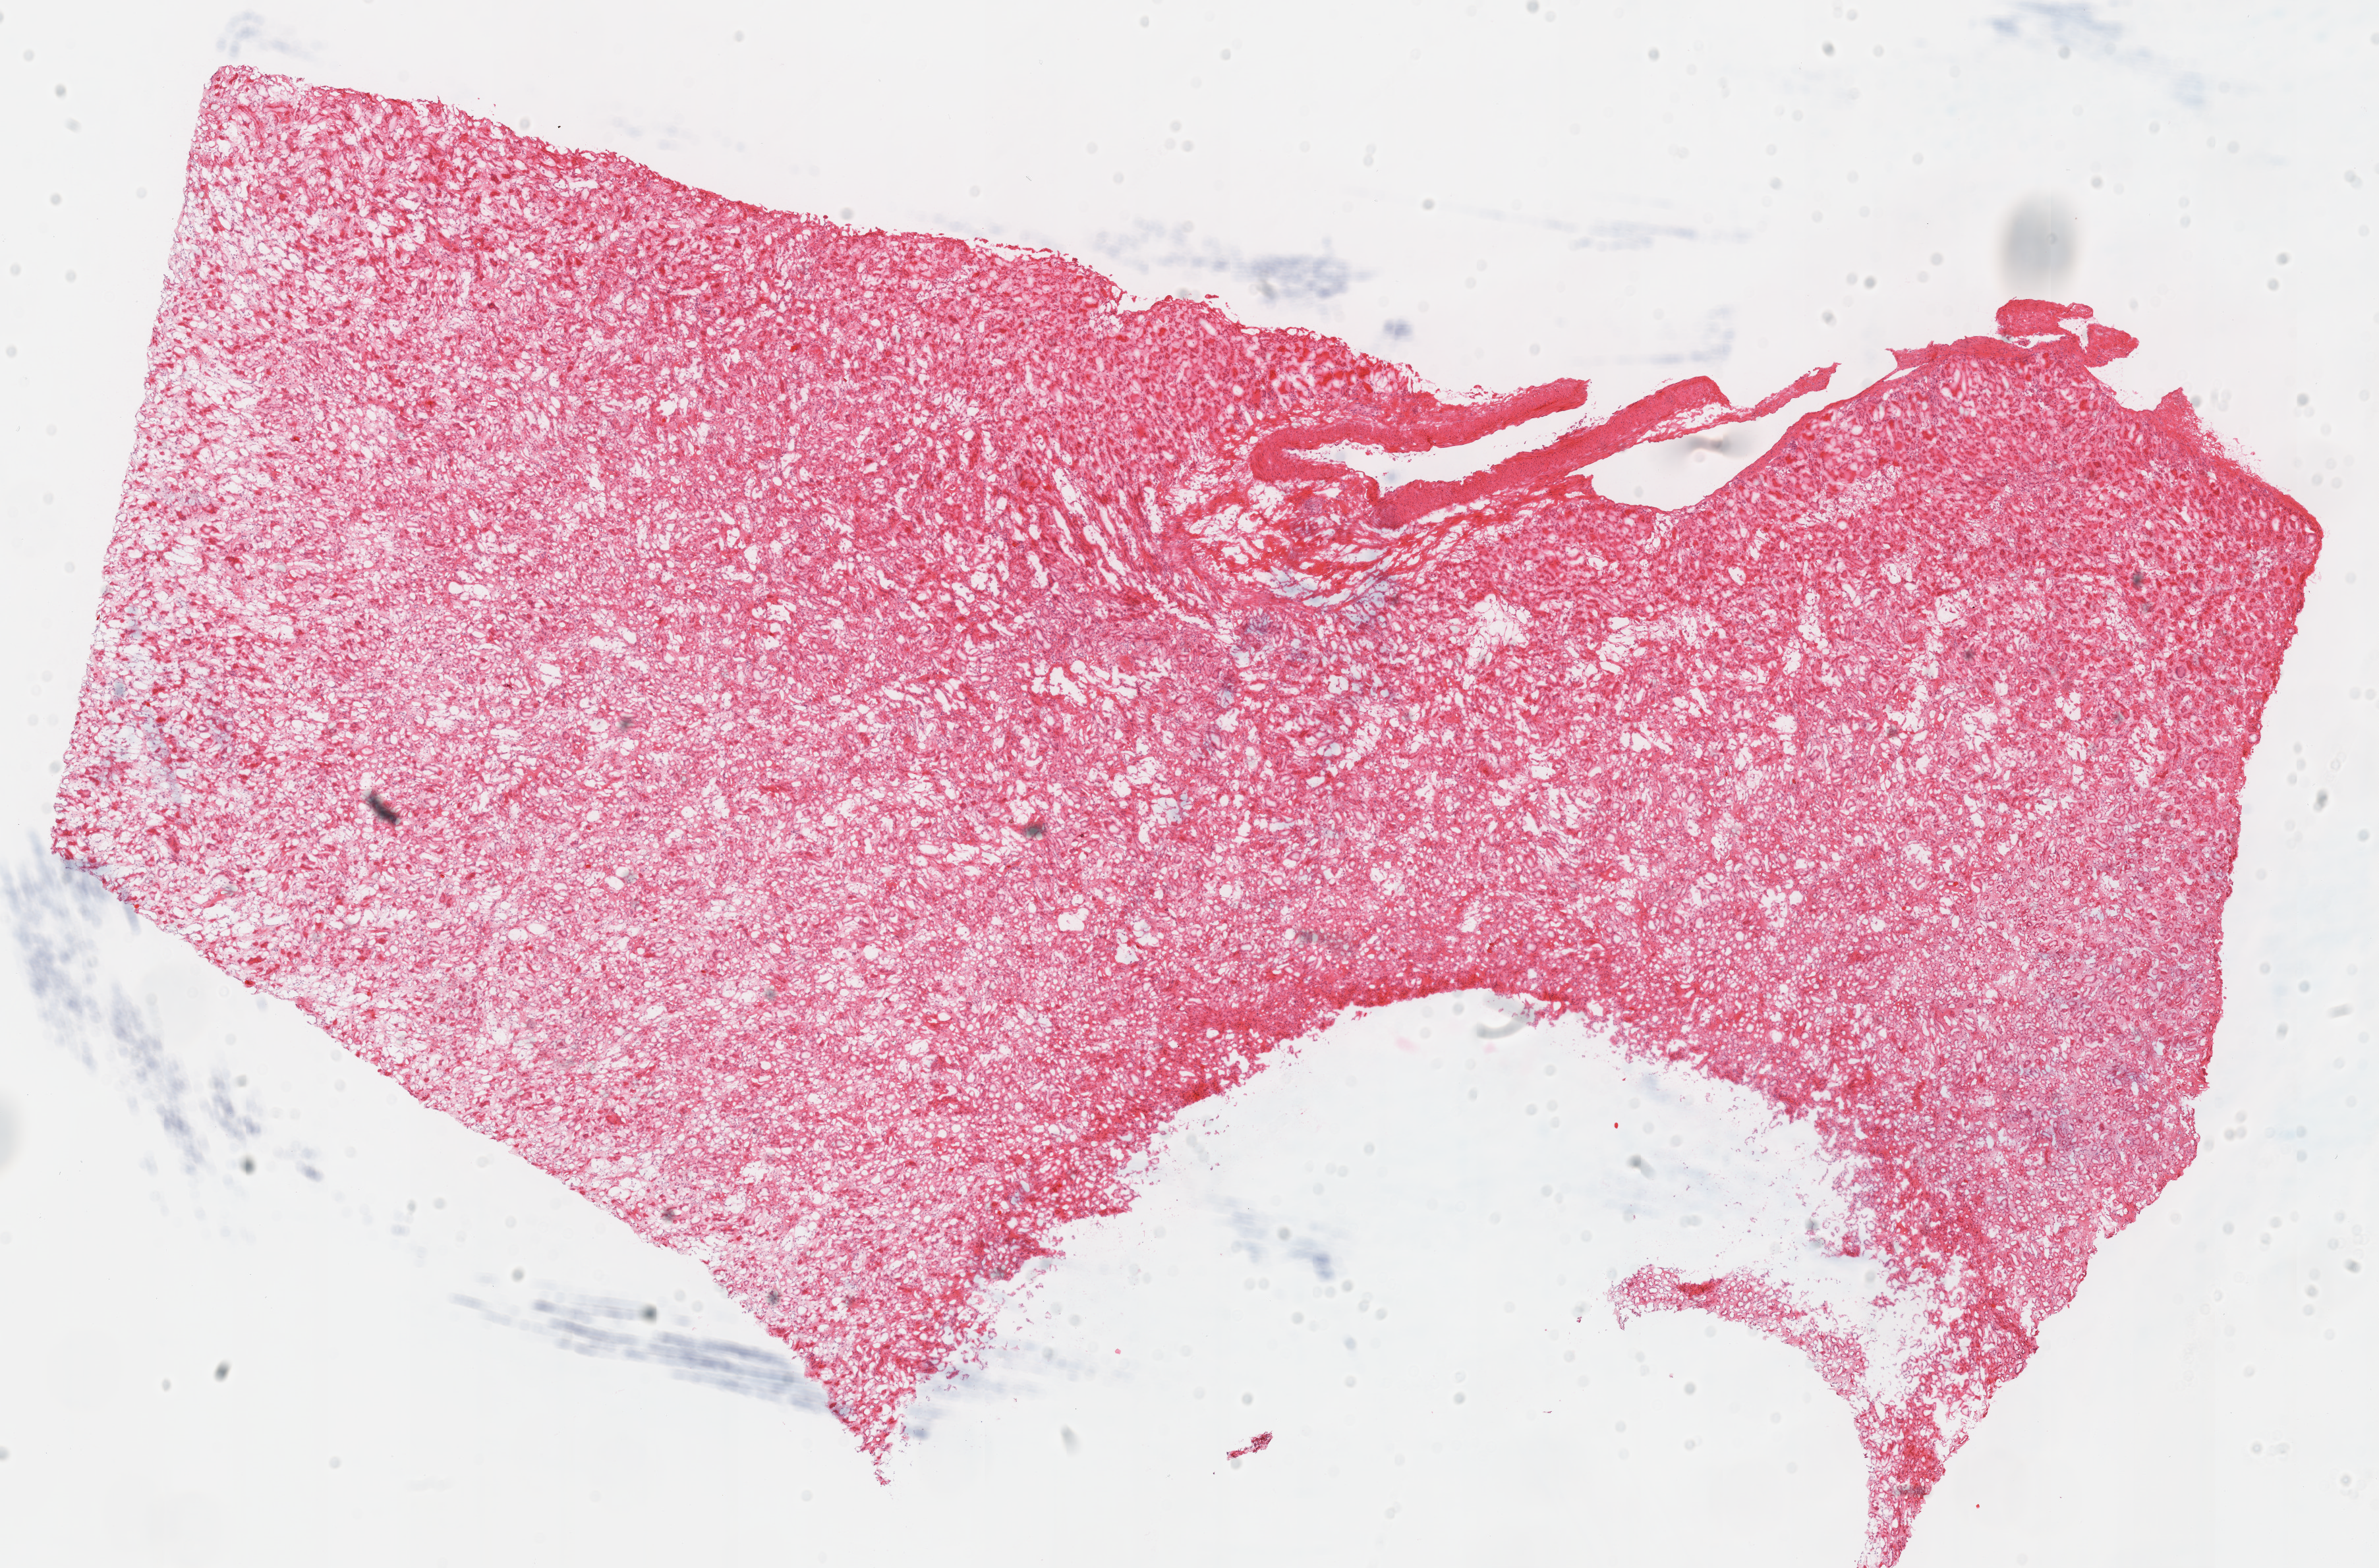
Digitized H&E tissue section (whole slide), shown as a low-resolution overview of the whole scanned area (about 14.2 x 9.4 mm, slide scanned at 40x), frozen section from the top of the tissue portion, kidney, solid tissue normal (non-tumour tissue) sample. Male, age 53 years at initial diagnosis. Inflammatory infiltration, as recorded: lymphocyte infiltration 0%, monocyte infiltration 0%, neutrophil infiltration 0%.
This section: solid tissue normal sample (biorepository sample class). Patient diagnosis: Renal cell carcinoma, chromophobe type.